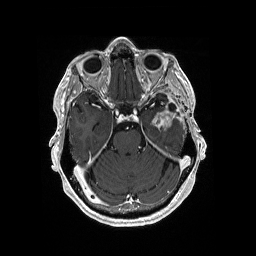
Brain MRI from a brain-tumour surgery series, one axial slice. Slice 121 of 176 in the series (ordered by position). T1-weighted post-contrast. 1 mm slice thickness. 256 × 256 image matrix, field of view 256 × 256 mm. From the clinical record (not read from this slice): histopathology: Glioblastoma; WHO grade: 4.
Structures marked on this image (expert manual segmentation):
- previous resection cavity: bounding box [x1, y1, x2, y2] px = [169, 104, 176, 111]
- tumour: [150, 112, 174, 130]